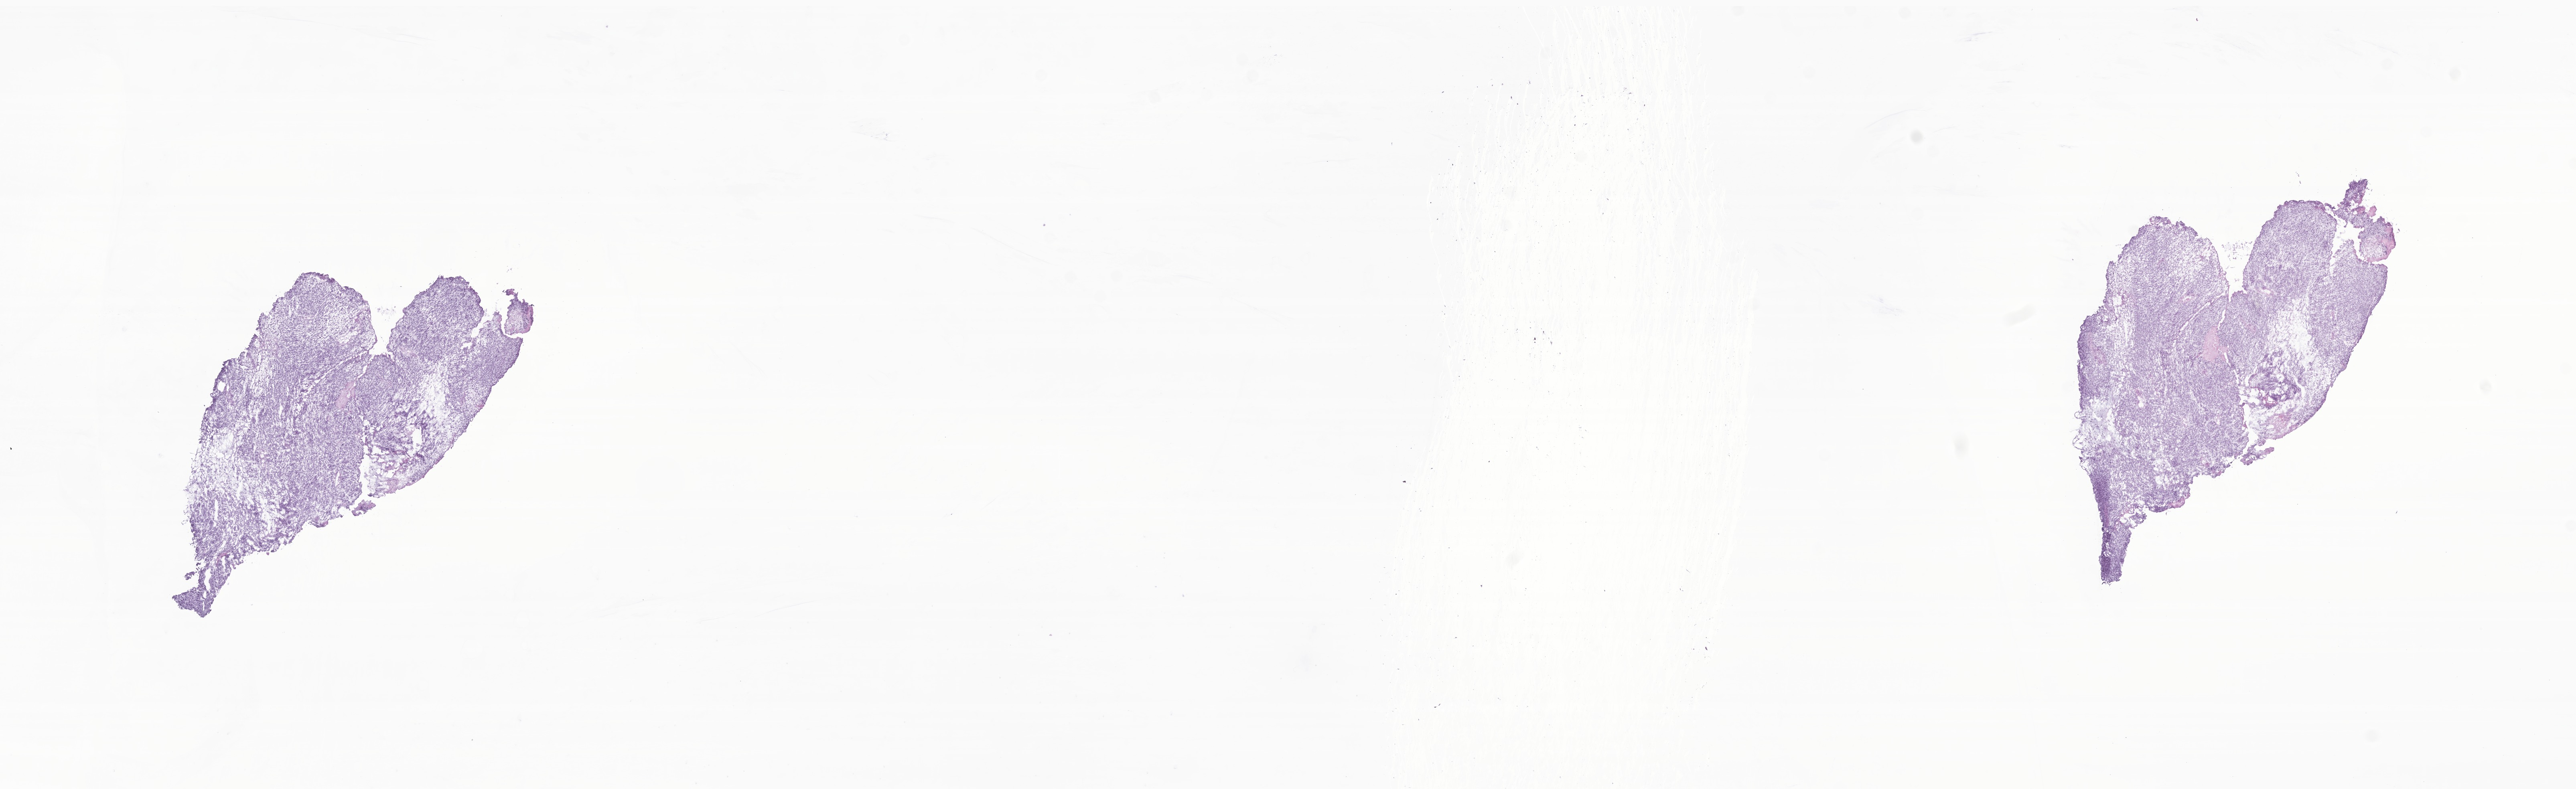
Digitized hematoxylin and eosin (H&E)-stained section of tumor tissue from the nasopharynx — whole scanned area (about 27.1 x 8.3 mm) shown as a low-resolution overview; frozen section. Patient: female, age 108 months (9 years).
Diagnosis: Neoplasm, uncertain whether benign or malignant.